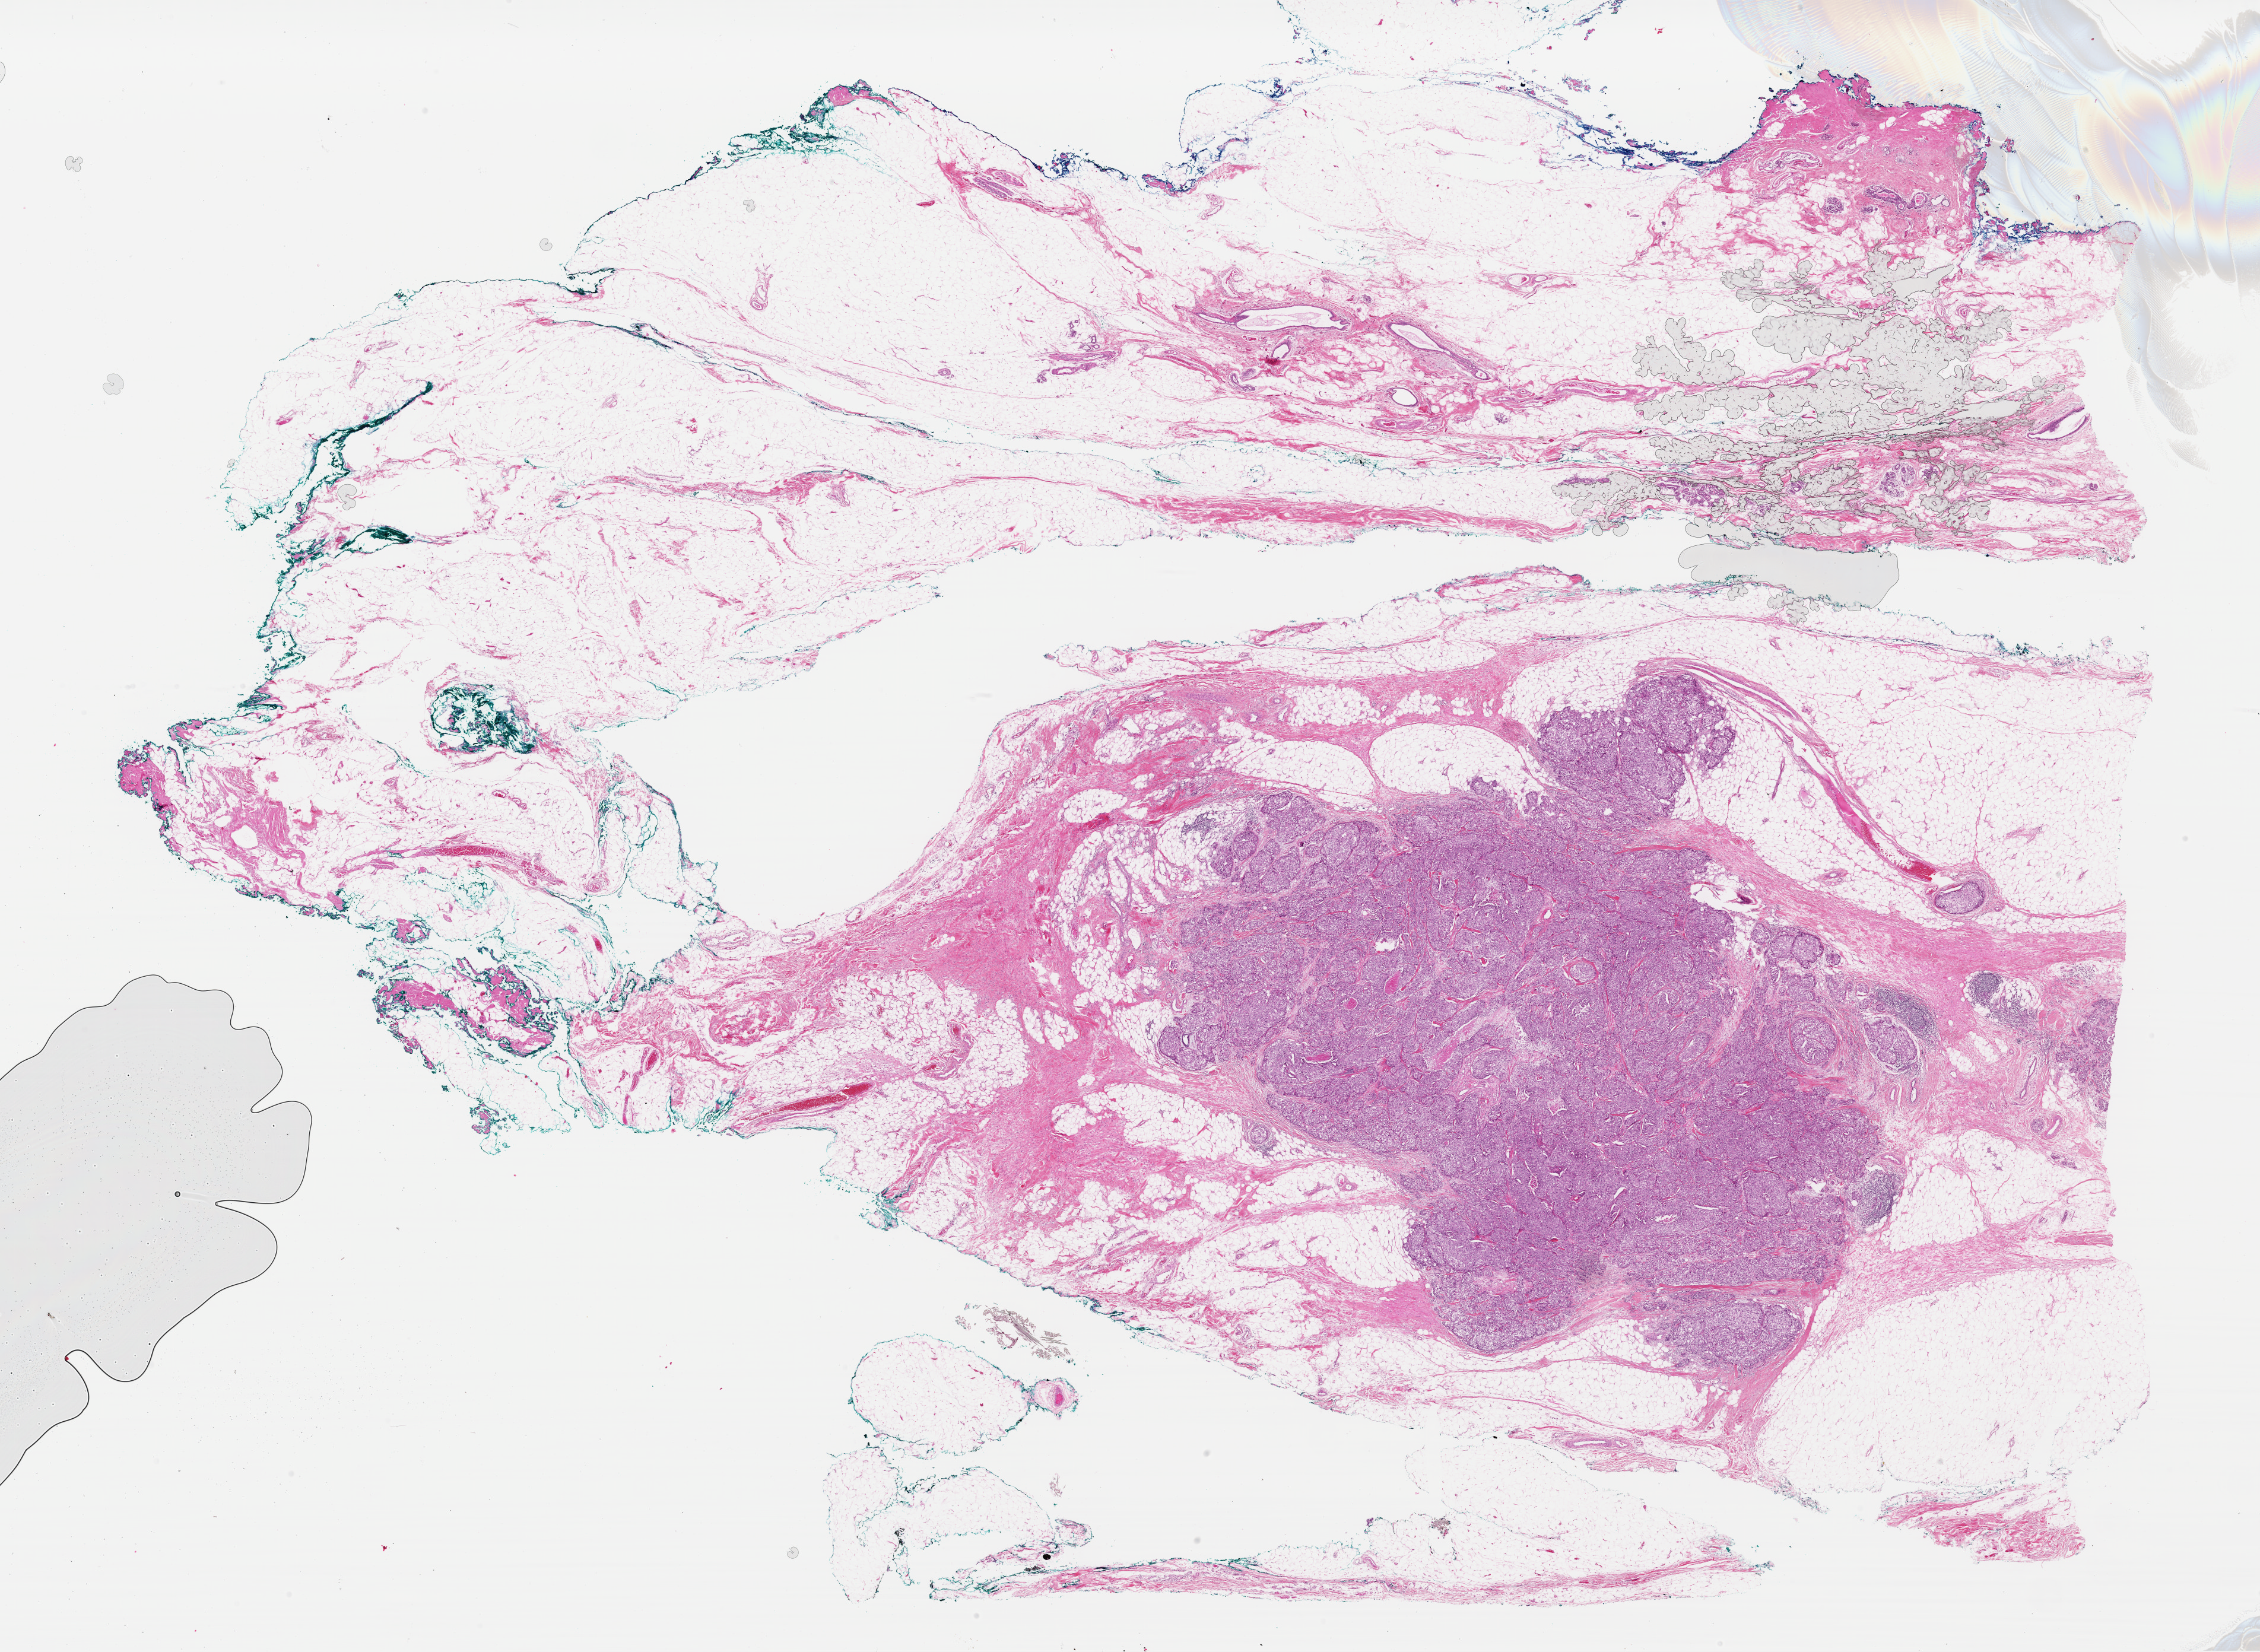
H&E-stained whole-slide image — whole scanned area (about 30.1 x 22.0 mm, acquisition: 40x scan) shown as a low-resolution overview. FFPE section. Primary tumour sample from the breast. Patient: female, age at initial diagnosis 68 years.
Pathologic diagnosis: Infiltrating duct carcinoma, NOS. AJCC pathologic stage: IIB. TNM: T2 N1 M0.